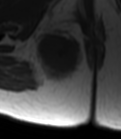
MRI of an extremity soft-tissue mass, one axial slice; position 26 of 47 along the scan axis; MR volume resampled by the dataset authors to the PET/CT grid (not the native acquisition matrix); 3.27 mm slice thickness; 121 × 139 image matrix. Female patient. From the clinical record (not read from this slice): histological type: epithelioid sarcoma; grade: intermediate; site of the primary tumour: right buttock.
Outlined on this slice (expert contour drawn on MRI and transferred to this co-registered scan by the dataset authors):
- gross tumour volume including surrounding oedema: box from (x=31, y=25) to (x=83, y=87) px
- gross tumour volume (mass): (x=36, y=34)–(x=81, y=80)